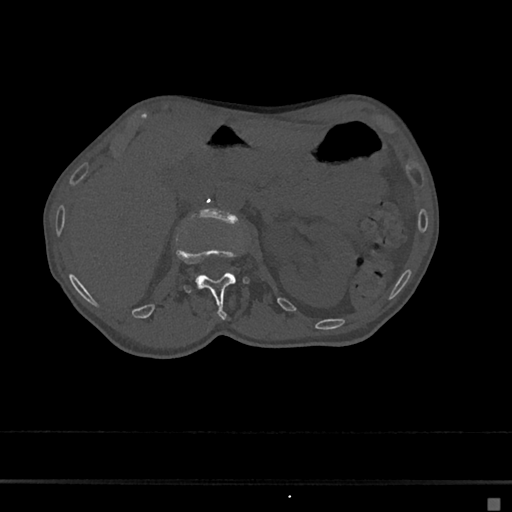
CT including the spine, one axial slice; slice 61 of 797 in the series (ordered by position); 120 kVp; bone window (W 1800 / L 400 HU); 0.5 mm slice thickness; 512 × 512 image matrix, field of view 360 × 360 mm. Female patient, age 68 years. From the clinical record (not read from this slice): primary cancer: renal.
Structures marked on this image (semi-automatically segmented with operator editing):
- L1 vertebra: box from (x=176, y=245) to (x=250, y=319) px
- L2 vertebra: (x=201, y=209)–(x=236, y=220)